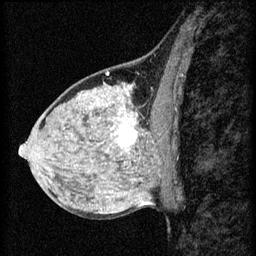
Breast MRI (dynamic contrast-enhanced), one sagittal slice. Position 31 of 60 along the scan axis. 3 images stored at this slice position (order not interpretable as contrast timing). 1.5 T. TE 4.2 ms, TR 8.2 ms. 2 mm slice thickness. 256 × 256 image matrix. Female patient, age 40 years.
Structures marked on this image (semi-automatically segmented with operator editing):
- analysis volume of interest (the breast-tissue region the enhancement analysis was run in; not a lesion): bounding box <108,108,167,159> (left, top, right, bottom; pixels)
- tumour enhancement mask (voxels above the 70 % enhancement threshold inside the analysis volume of interest): <112,120,137,147>